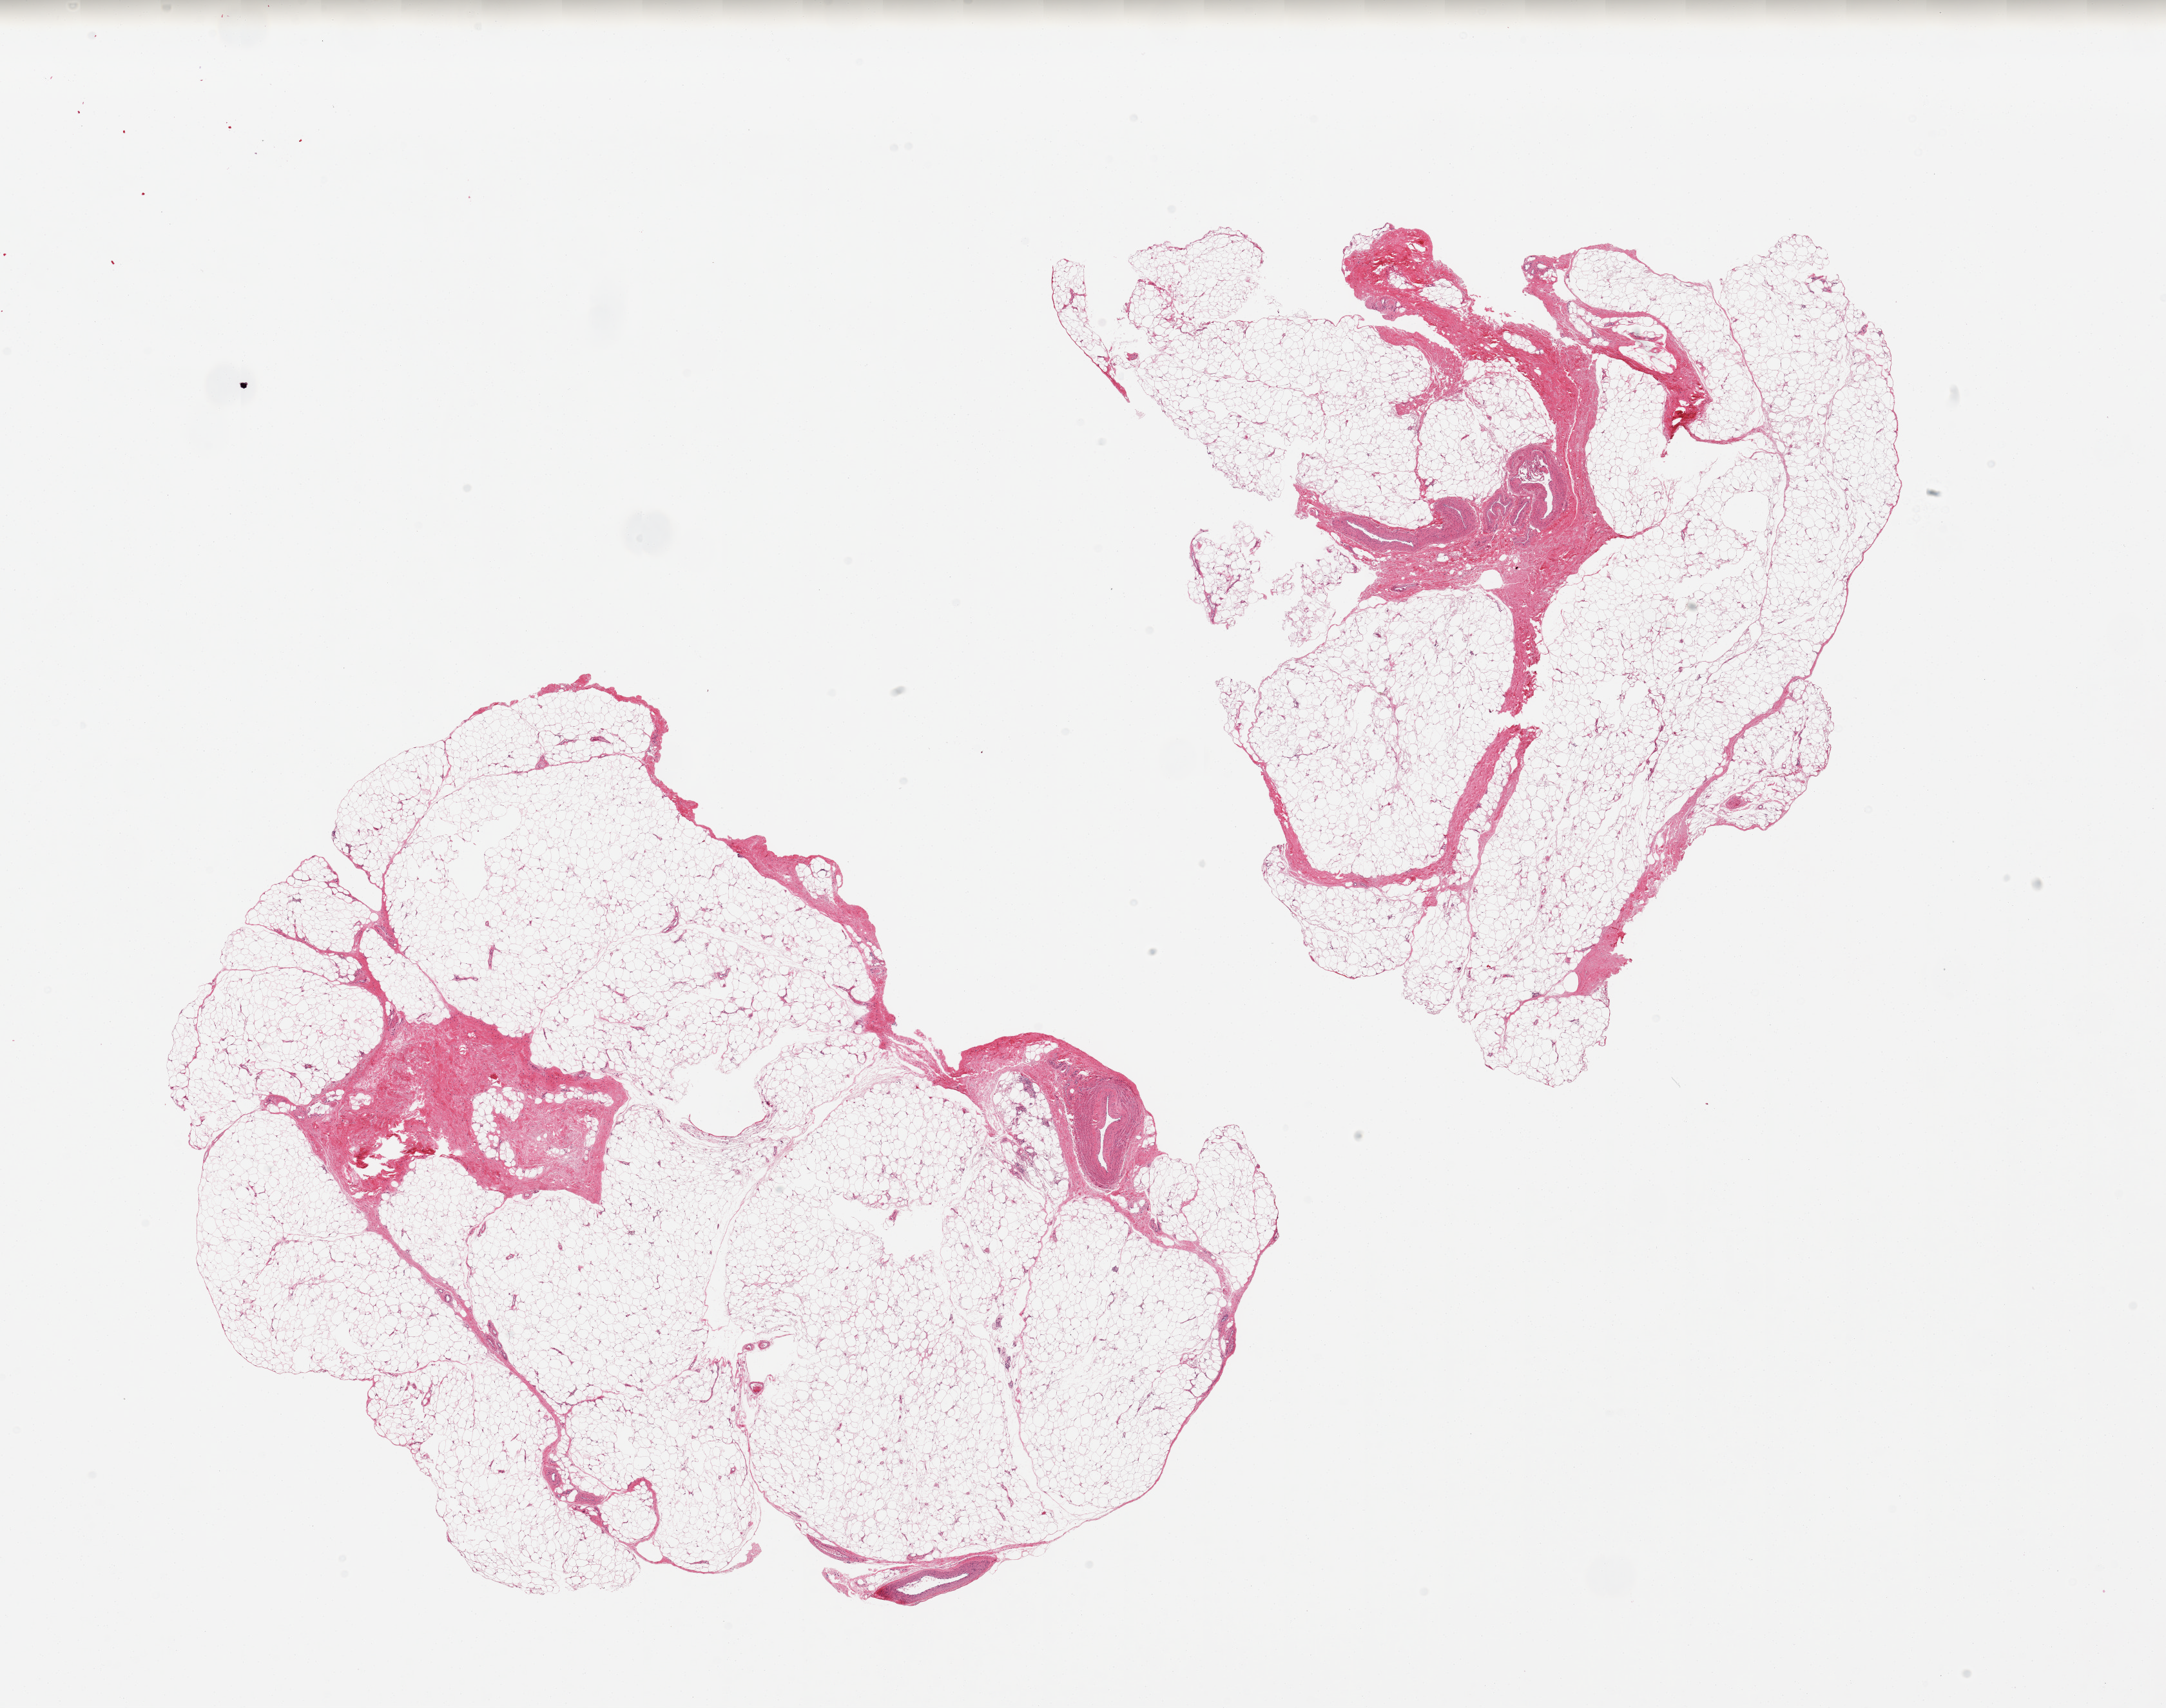
Digitized hematoxylin and eosin (H&E)-stained section — low-resolution overview of the scanned area, about 26.6 x 21.0 mm, PAXgene-fixed, paraffin-embedded tissue, target tissue: adipose tissue, donor tissue sample. Donor: male.
Pathologist's review note for this sample: 2 pieces, ~15% interstitial fascia/vascular elements.